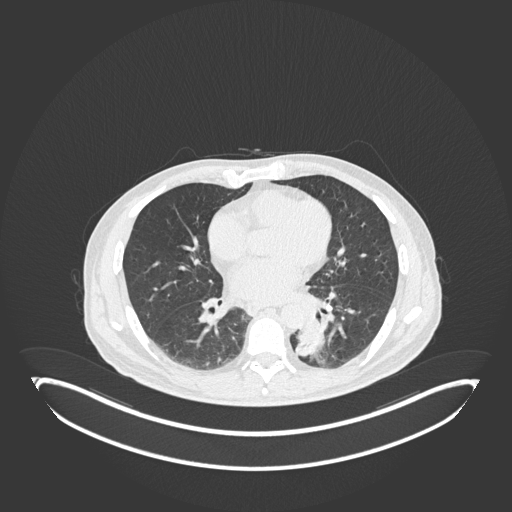
Chest CT, one axial slice. Position 76 of 251 along the scan axis. Reconstruction kernel B30f. Lung window (W 1500 / L -600 HU). 512 × 512 image matrix. Patient: male, 72 years. From the clinical record (not read from this slice): clinical TNM (as recorded): T2b N0 M1.
Structures marked on this image (rectangle marked by the reading radiologist):
- lung tumour (recorded histology: adenocarcinoma): box from (x=294, y=320) to (x=326, y=360) px